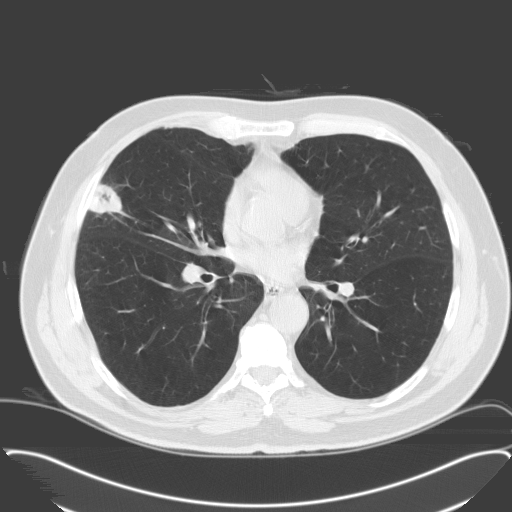
Low-dose screening chest CT, one axial slice; position 91 of 174 along the scan axis; lung window (W 1500 / L -600 HU); 3.2 mm slice thickness; 512 × 512 image matrix.
Structures marked on this image (expert manual segmentation):
- lesion 1 (tumor, middle lobe of right lung): bounding box (x1, y1, x2, y2) in pixels: (88, 184, 122, 214)